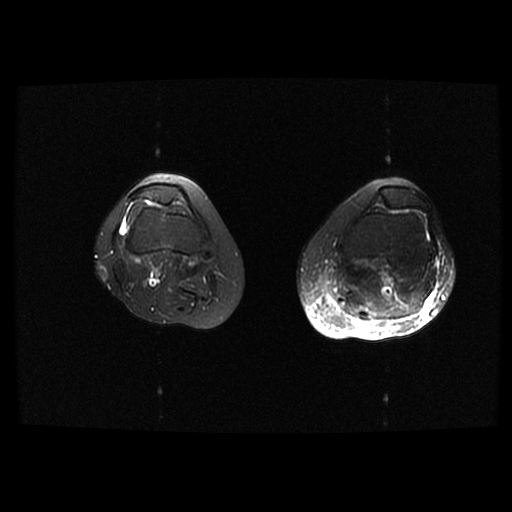
MRI of an extremity soft-tissue mass, one axial slice. Position 11 of 42 along the scan axis. T2-weighted fat-saturated. 6 mm slice thickness. 512 × 512 image matrix, field of view 420 × 420 mm. Female patient. Case-level facts recorded for this patient, not image findings: histological type: pleomorphic leiomyosarcoma; grade: high; site of the primary tumour: left thigh.
Annotated regions visible in this slice (expert manual segmentation):
- gross tumour volume including surrounding oedema: bounding box [x1, y1, x2, y2] px = [323, 267, 342, 304]